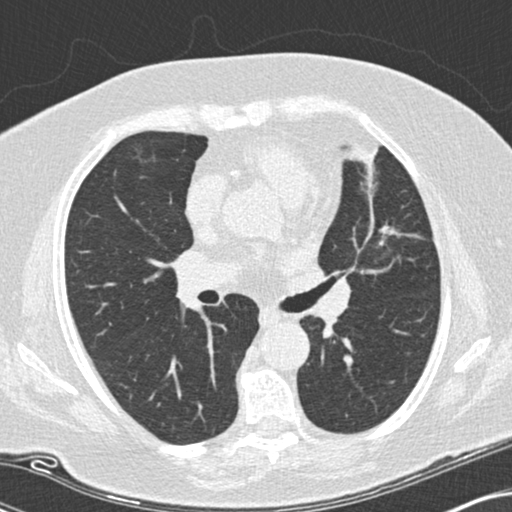
Low-dose screening chest CT, one axial slice. Reconstruction kernel B30f. 120 kVp. Lung window (W 1500 / L -600 HU). 2 mm slice thickness. 512 × 512 image matrix, field of view 330 × 330 mm.
Annotated regions visible in this slice (expert manual segmentation):
- lesion 1 (tumor, upper lobe of left lung): bounding box (x1, y1, x2, y2) in pixels: (380, 225, 401, 236)